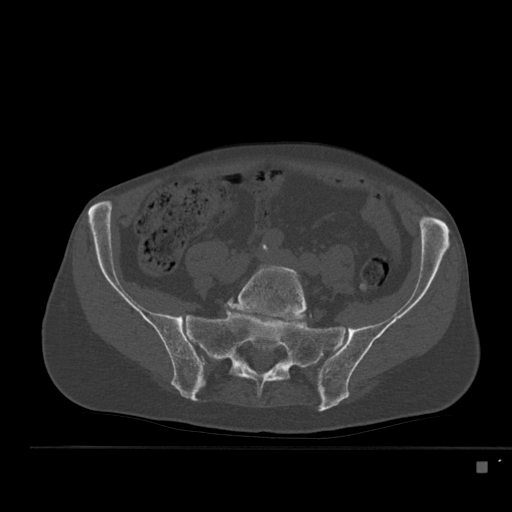
CT including the spine, one axial slice; slice 113 of 517 in the series (ordered by position); bone window (W 1800 / L 400 HU); 1.5 mm slice thickness; 512 × 512 image matrix, field of view 408 × 408 mm. Patient: male, 70 years. Case-level facts recorded for this patient, not image findings: primary cancer: renal; vertebrae with lytic lesions (as recorded): T4, T6, T10, T12, L3, L4, L5.
Annotated regions visible in this slice (semi-automatic segmentation, software-assisted and operator-edited):
- L5 vertebra: box from (x=227, y=264) to (x=311, y=323) px